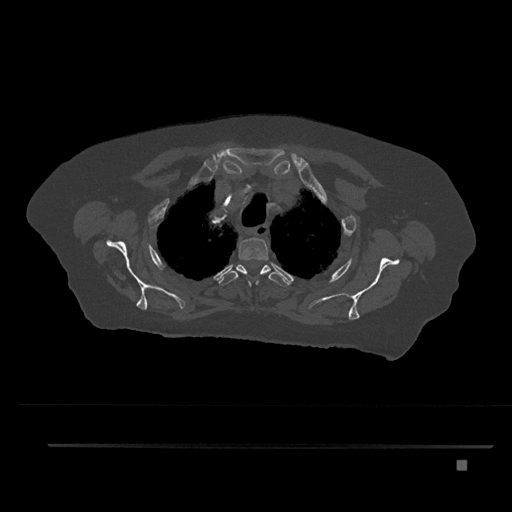
CT including the spine, one axial slice; position 651 of 797 along the scan axis; 120 kVp; bone window (W 1800 / L 400 HU); 0.5 mm slice thickness; 512 × 512 image matrix, field of view 437 × 437 mm. Female patient, age 76 years. From the clinical record (not read from this slice): primary cancer: lung.
Annotated regions visible in this slice (semi-automatic segmentation, software-assisted and operator-edited):
- T2 vertebra: bounding box <238,237,271,286> (left, top, right, bottom; pixels)
- T3 vertebra: <218,264,289,287>